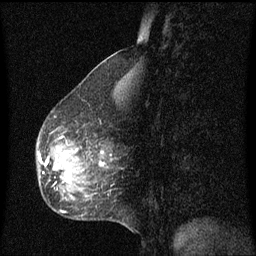
Breast MRI (dynamic contrast-enhanced), one sagittal slice; dynamic contrast-enhanced series, image 2 of 3 at this slice position (ordered by acquisition); 1.5 T; TE 4.2 ms, TR 8.4 ms; 2 mm slice thickness; 256 × 256 image matrix, field of view 200 × 200 mm. Female patient, age 49 years. Case-level facts recorded for this patient, not image findings: setting: breast cancer imaged before/during neoadjuvant chemotherapy; receptor status: HR-positive, HER2-negative.
Outlined on this slice (semi-automatically segmented with operator editing):
- analysis volume of interest (the breast-tissue region the enhancement analysis was run in; not a lesion): box from (x=37, y=130) to (x=115, y=201) px
- tumour enhancement mask (voxels above the 70 % enhancement threshold inside the analysis volume of interest): (x=59, y=152)–(x=70, y=181)